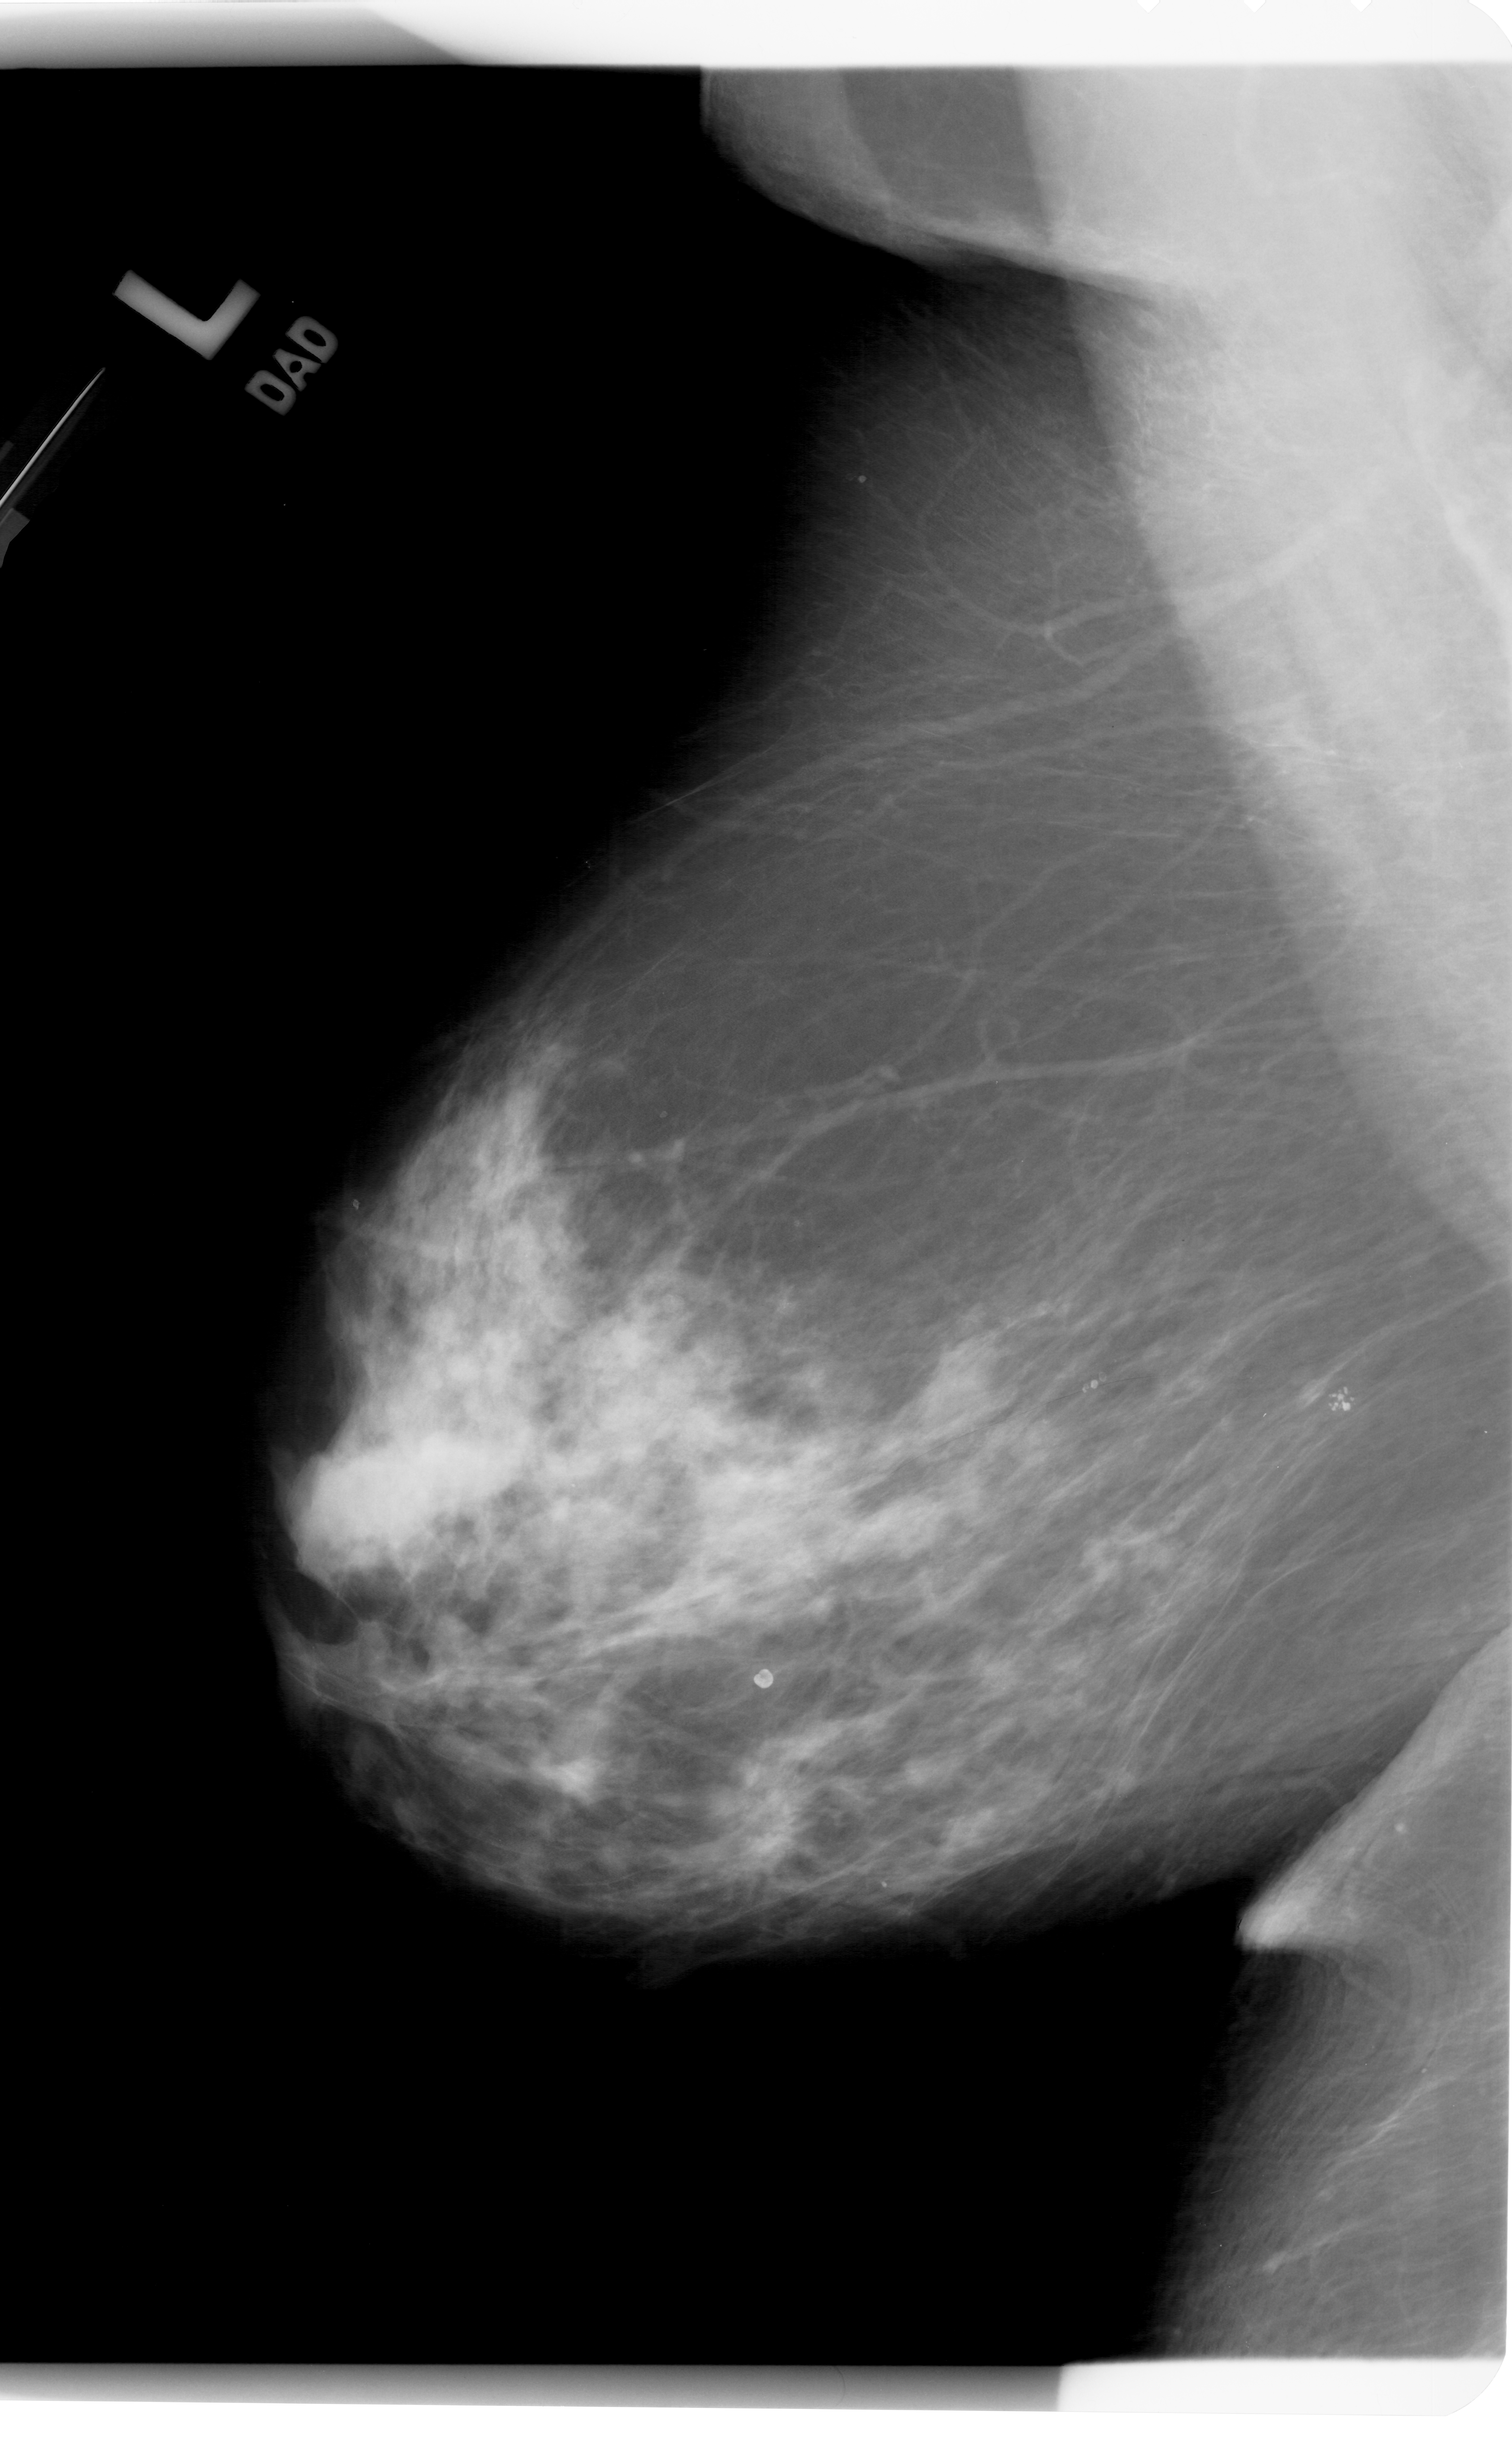
Mammogram (digitized film); left breast; MLO view; breast composition: heterogeneously dense (BI-RADS density category 3 of 4); 1512 × 2456 image matrix.
Expert-marked regions of interest on this film, with their recorded descriptors:
- mass, shape architectural distortion, margins spiculated; BI-RADS assessment category 5; pathology (as recorded): malignant: bounding box [x1, y1, x2, y2] px = [702, 1784, 813, 1890]